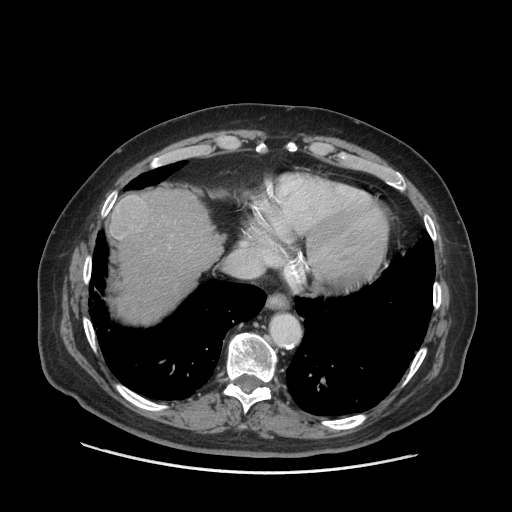
Contrast-enhanced abdominal CT (liver protocol), one axial slice. Position 62 of 77 along the scan axis. Soft-tissue window (W 400 / L 40 HU). 2.5 mm slice thickness. 512 × 512 image matrix. From the clinical record (not read from this slice): diagnosis: hepatocellular carcinoma (patient treated with transarterial chemoembolisation; whether this scan precedes or follows treatment is not stated here); TNM stage (as recorded): Stage-I; Child-Pugh class: A; tumour differentiation: well differentiated; tumour size: 3.8 cm.
Outlined on this slice (semi-automatic segmentation, software-assisted and operator-edited):
- abdominal aorta: bounding box <271,315,300,344> (left, top, right, bottom; pixels)
- liver parenchyma outside the tumour (the mass and vessels are separate outlines, so this box may not span the whole liver): <108,188,222,322>
- mass: <109,195,149,239>